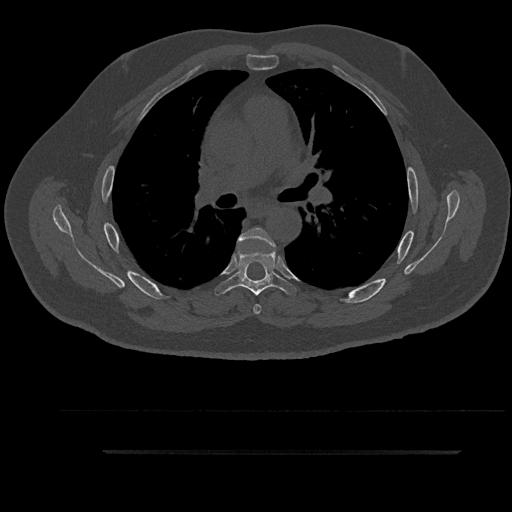
CT including the spine, one axial slice; slice 592 of 797 in the series (ordered by position); 120 kVp; bone window (W 1800 / L 400 HU); 512 × 512 image matrix, field of view 432 × 432 mm. Patient: male, 63 years. Case-level facts recorded for this patient, not image findings: primary cancer: renal; vertebrae with lytic lesions (as recorded): T8.
Structures marked on this image (semi-automatic segmentation, software-assisted and operator-edited):
- T5 vertebra: bounding box [x1, y1, x2, y2] px = [237, 227, 275, 314]
- T6 vertebra: [218, 242, 289, 296]